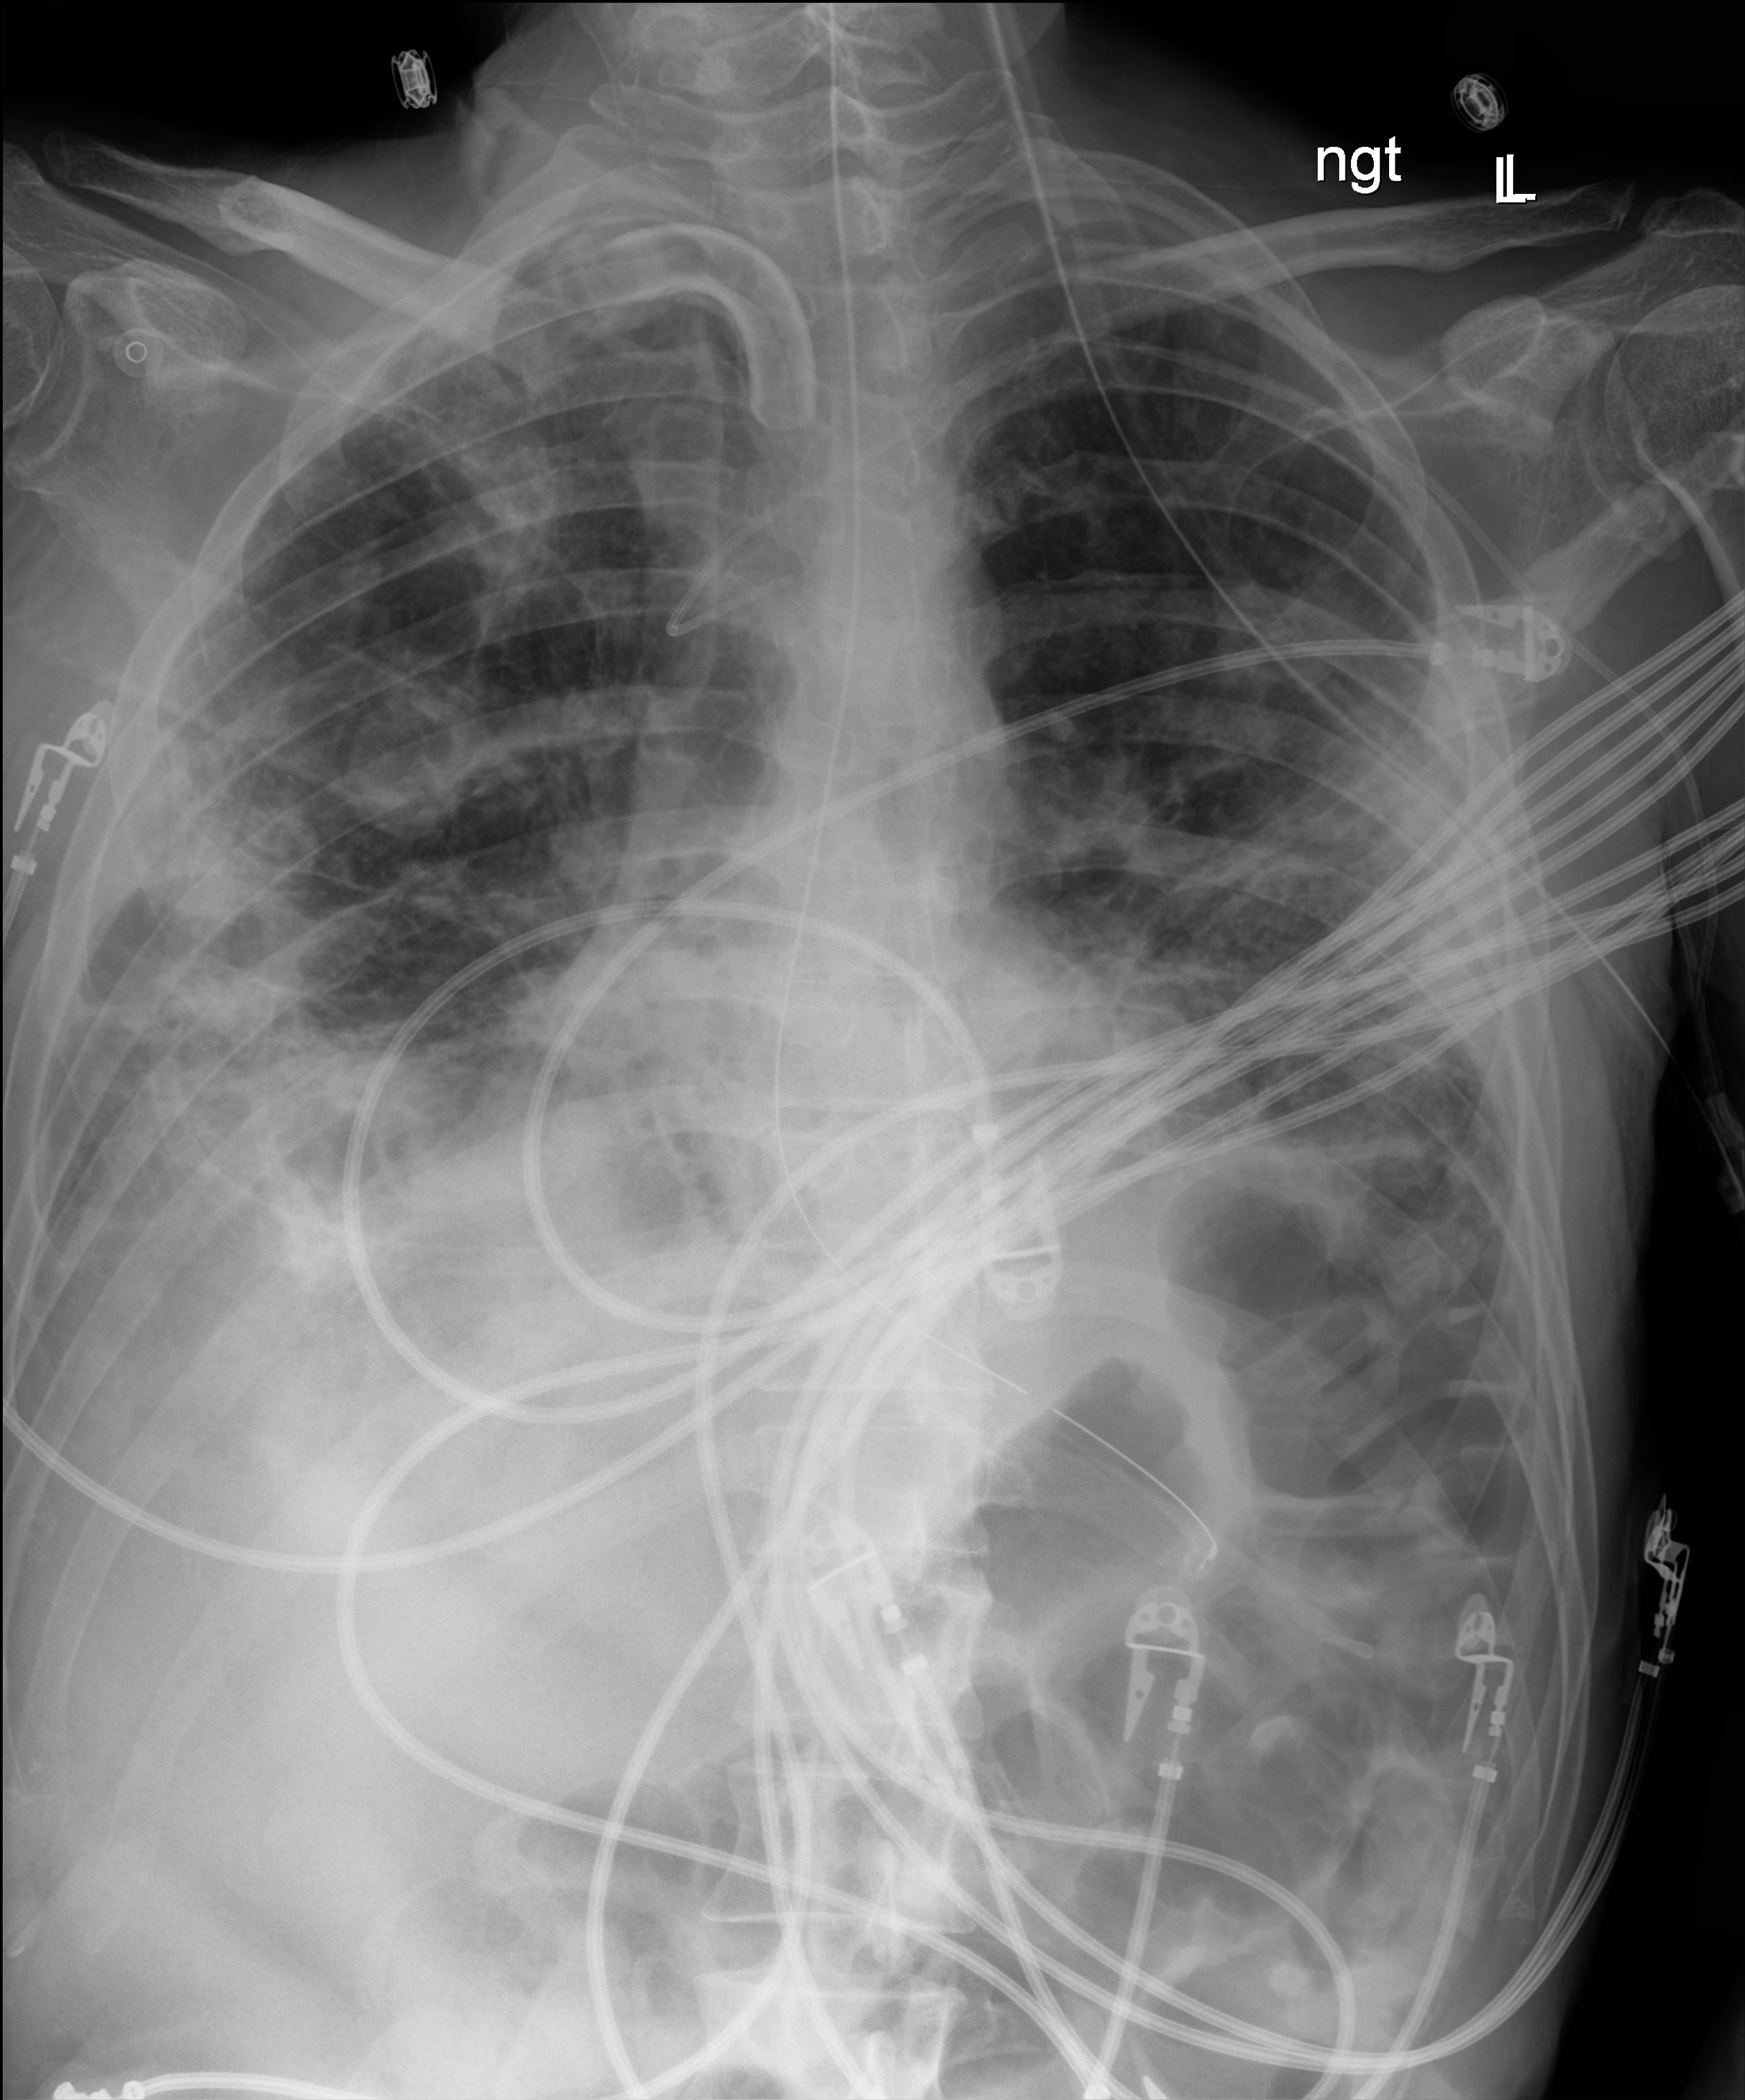
Chest X-ray (portable); anteroposterior (AP) projection. Male patient hospitalised with COVID-19, age 18–59 years.
From the hospital-stay record, not from the radiograph (when in the stay this image was taken is not recorded):
- admitted to intensive care during this hospital stay: yes
- mechanically ventilated during this hospital stay: yes
- COPD (admission record): no